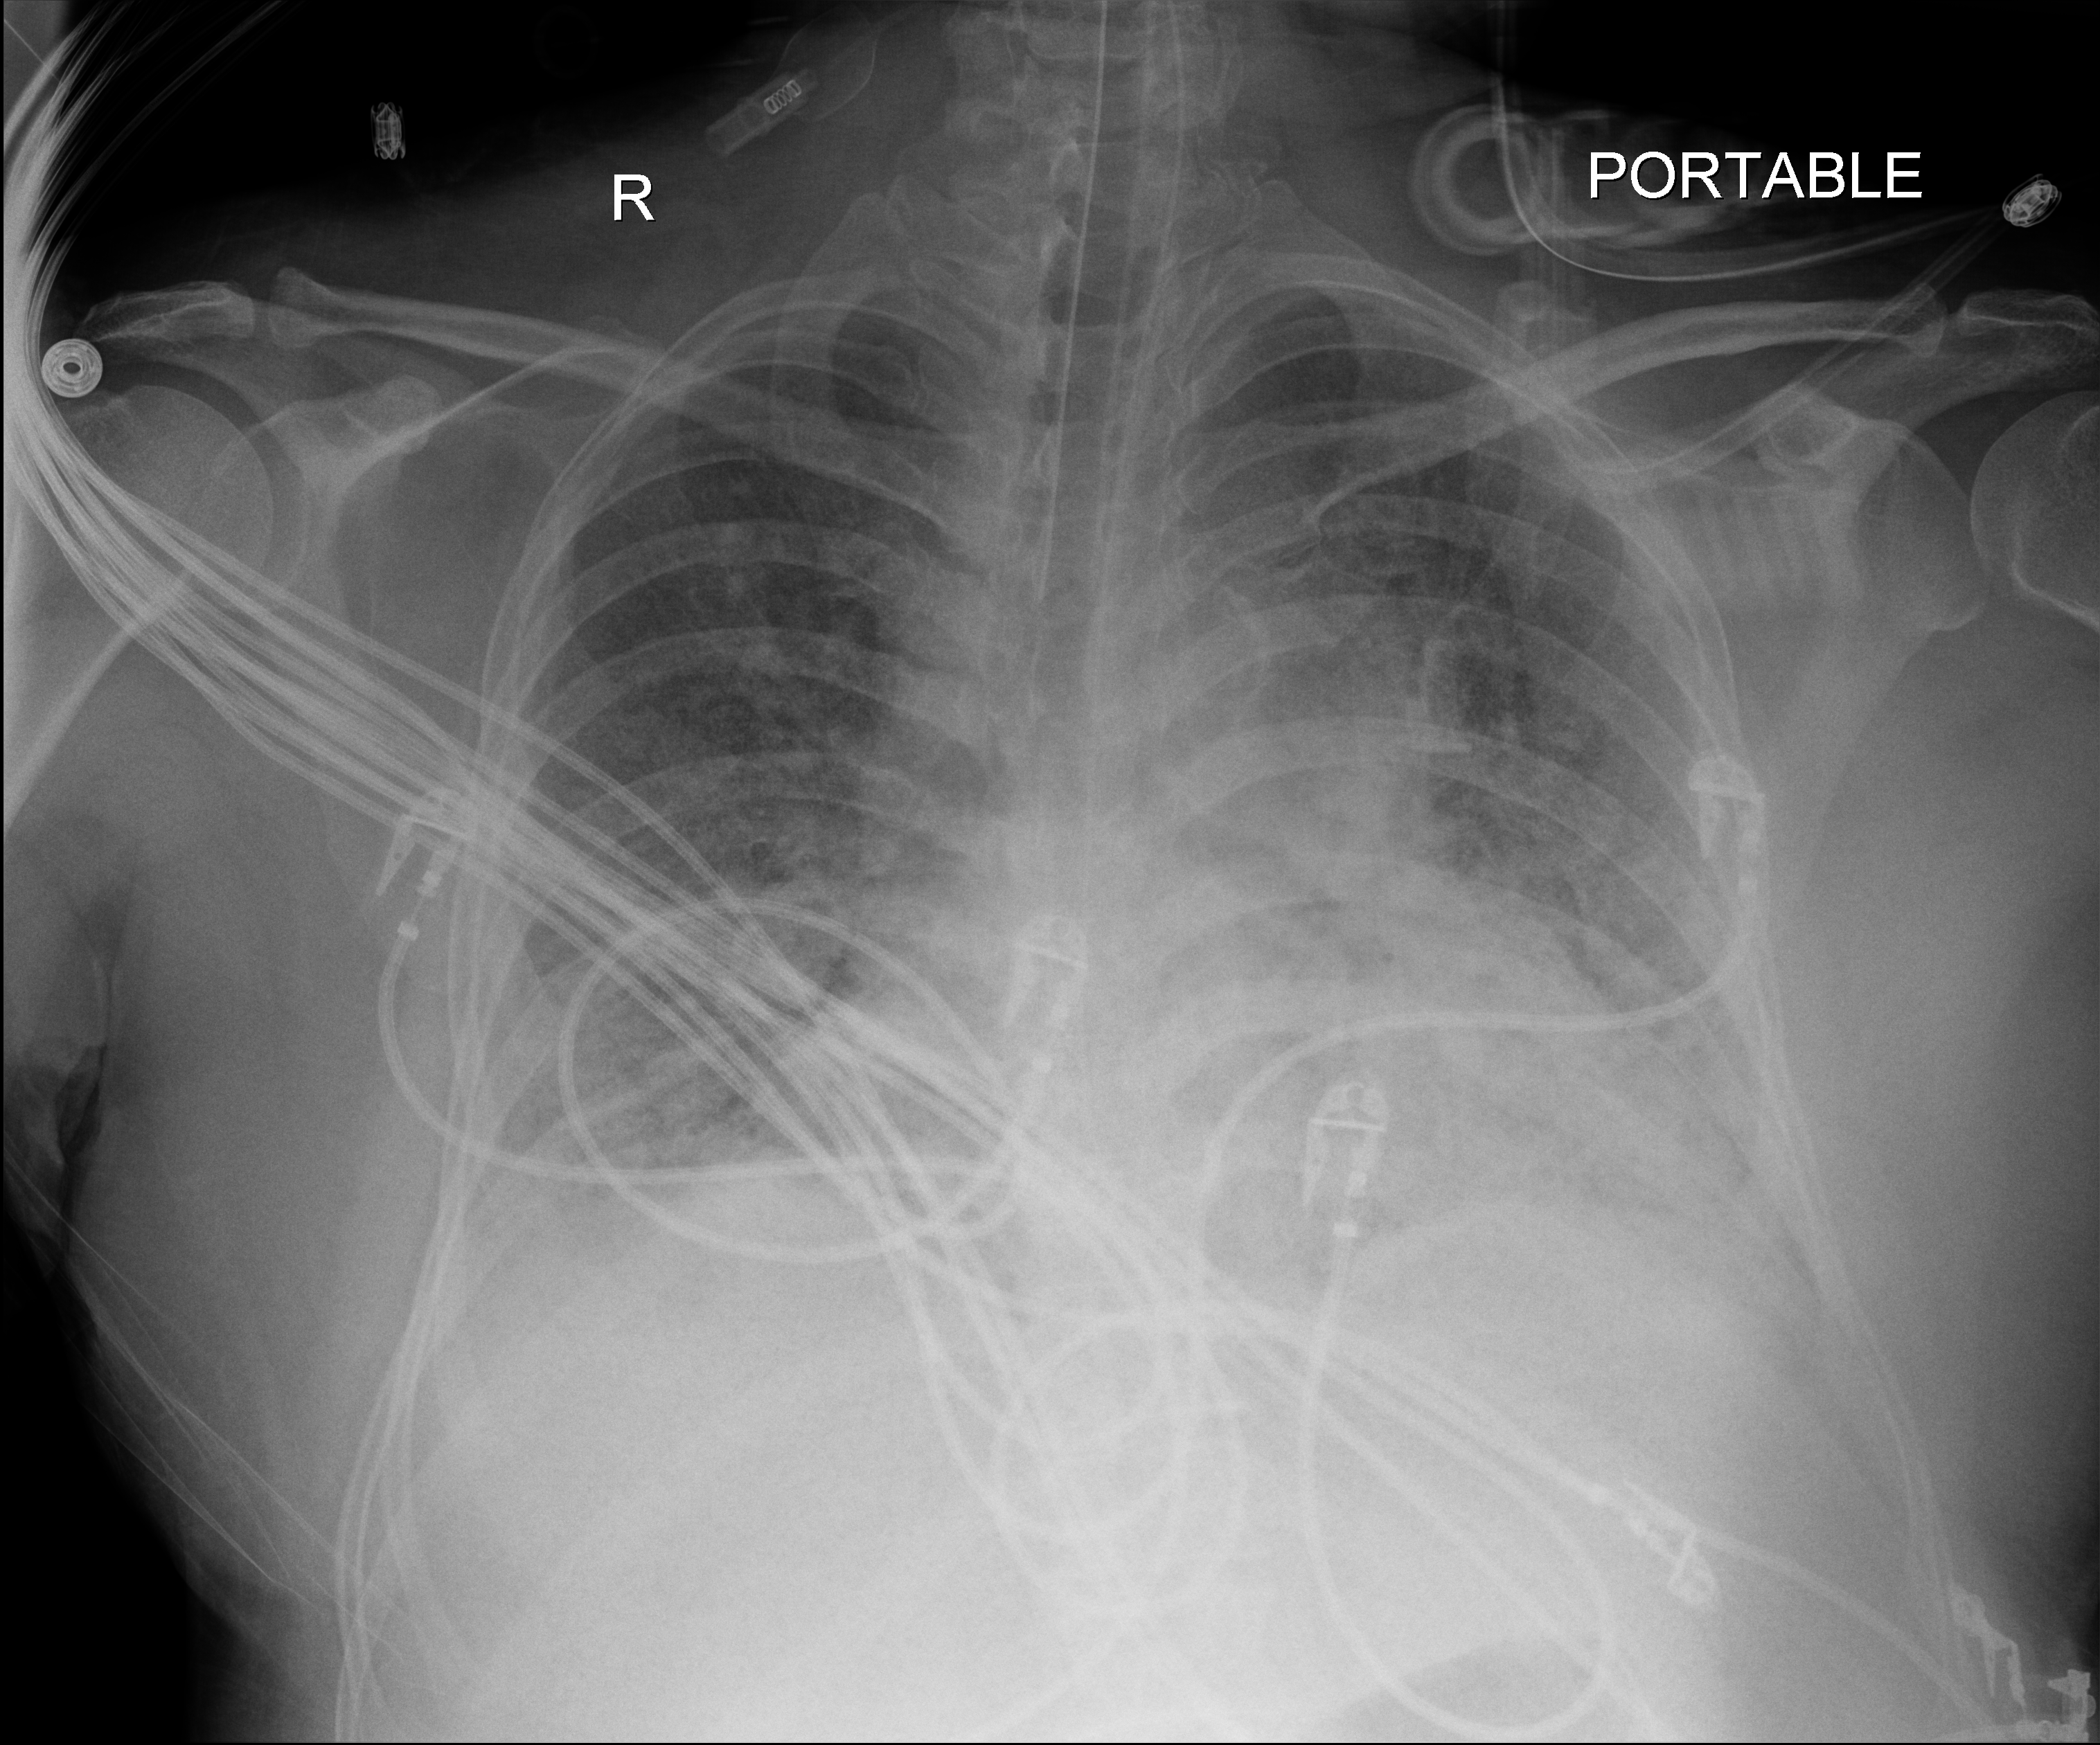
Portable chest radiograph; anteroposterior (AP) projection. Adult patient hospitalised with COVID-19, age 18–59 years.
Admission-level facts for this patient (not findings on this image; timing relative to this image not recorded): hypertension (admission record): no.